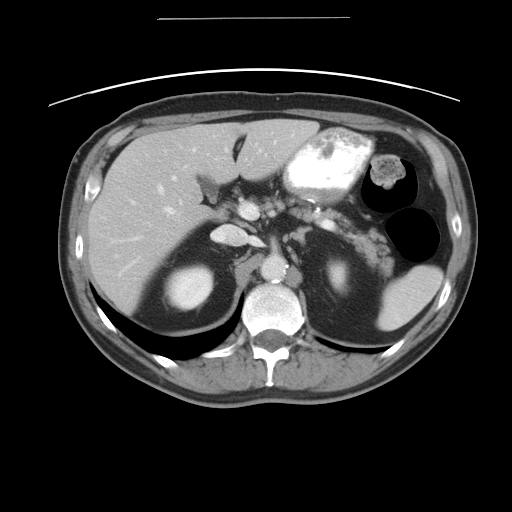
Contrast-enhanced abdominal CT, one axial slice; slice 27 of 49 in the series (ordered by position); reconstruction kernel STANDARD; 120 kVp; intravenous contrast given; soft-tissue window (W 400 / L 40 HU); 5 mm slice thickness; 512 × 512 image matrix. Male patient, age 57 years. Case-level facts recorded for this patient, not image findings: diagnosis: colorectal cancer liver metastases, imaged before liver resection; multiple liver metastases: yes; largest metastasis: 4 cm; disease in both lobes: no.
Outlined on this slice (expert manual segmentation):
- hepatic veins: bounding box (x1, y1, x2, y2) in pixels: (114, 147, 194, 256)
- liver: (88, 119, 318, 314)
- planned liver remnant (the part of the liver to remain after resection): (211, 119, 318, 182)
- portal vein (with intrahepatic branches): (110, 147, 227, 276)